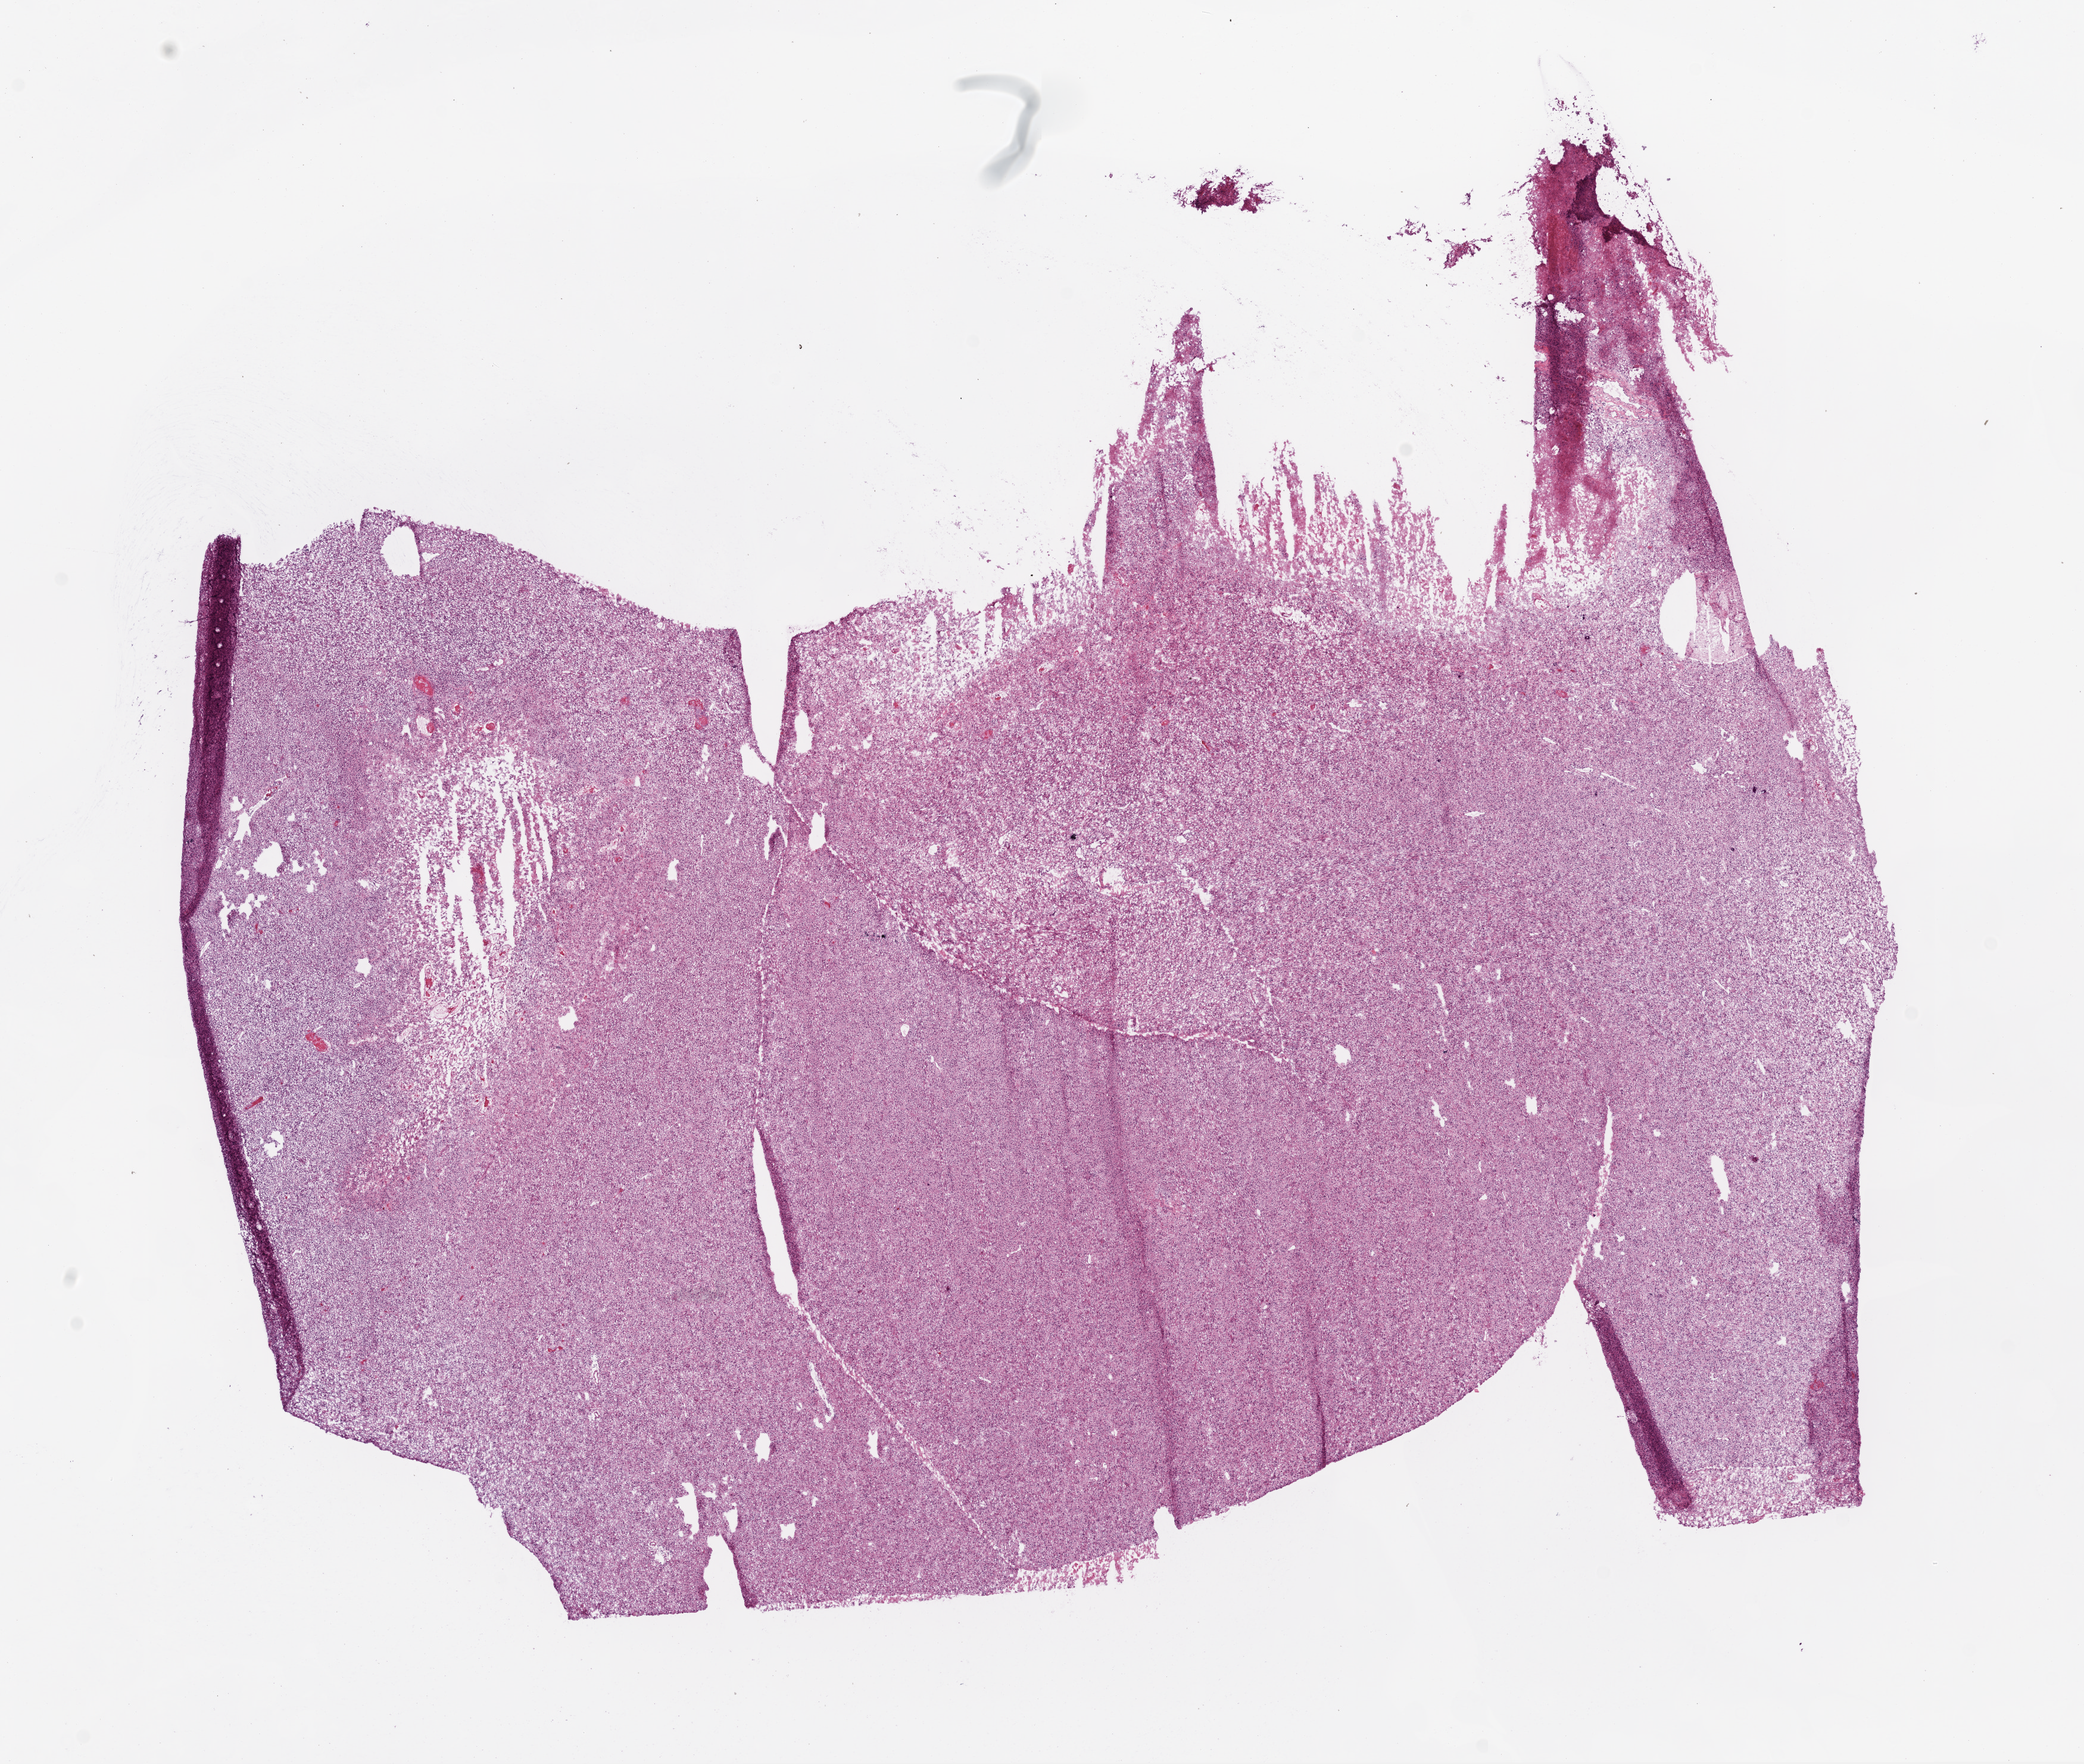
H&E whole-slide image, whole scanned area (about 14.0 x 11.9 mm, slide scanned at 20x) shown as a low-resolution overview. Frozen section. Sample: primary tumour, brain. Female, age 74 years at initial diagnosis. Pathologist review of this section (percent, as recorded): tumour cells 90%, tumour nuclei 85%, normal cells 0%, stromal cells 0%, necrosis 10%.
Histologic diagnosis: Glioblastoma.